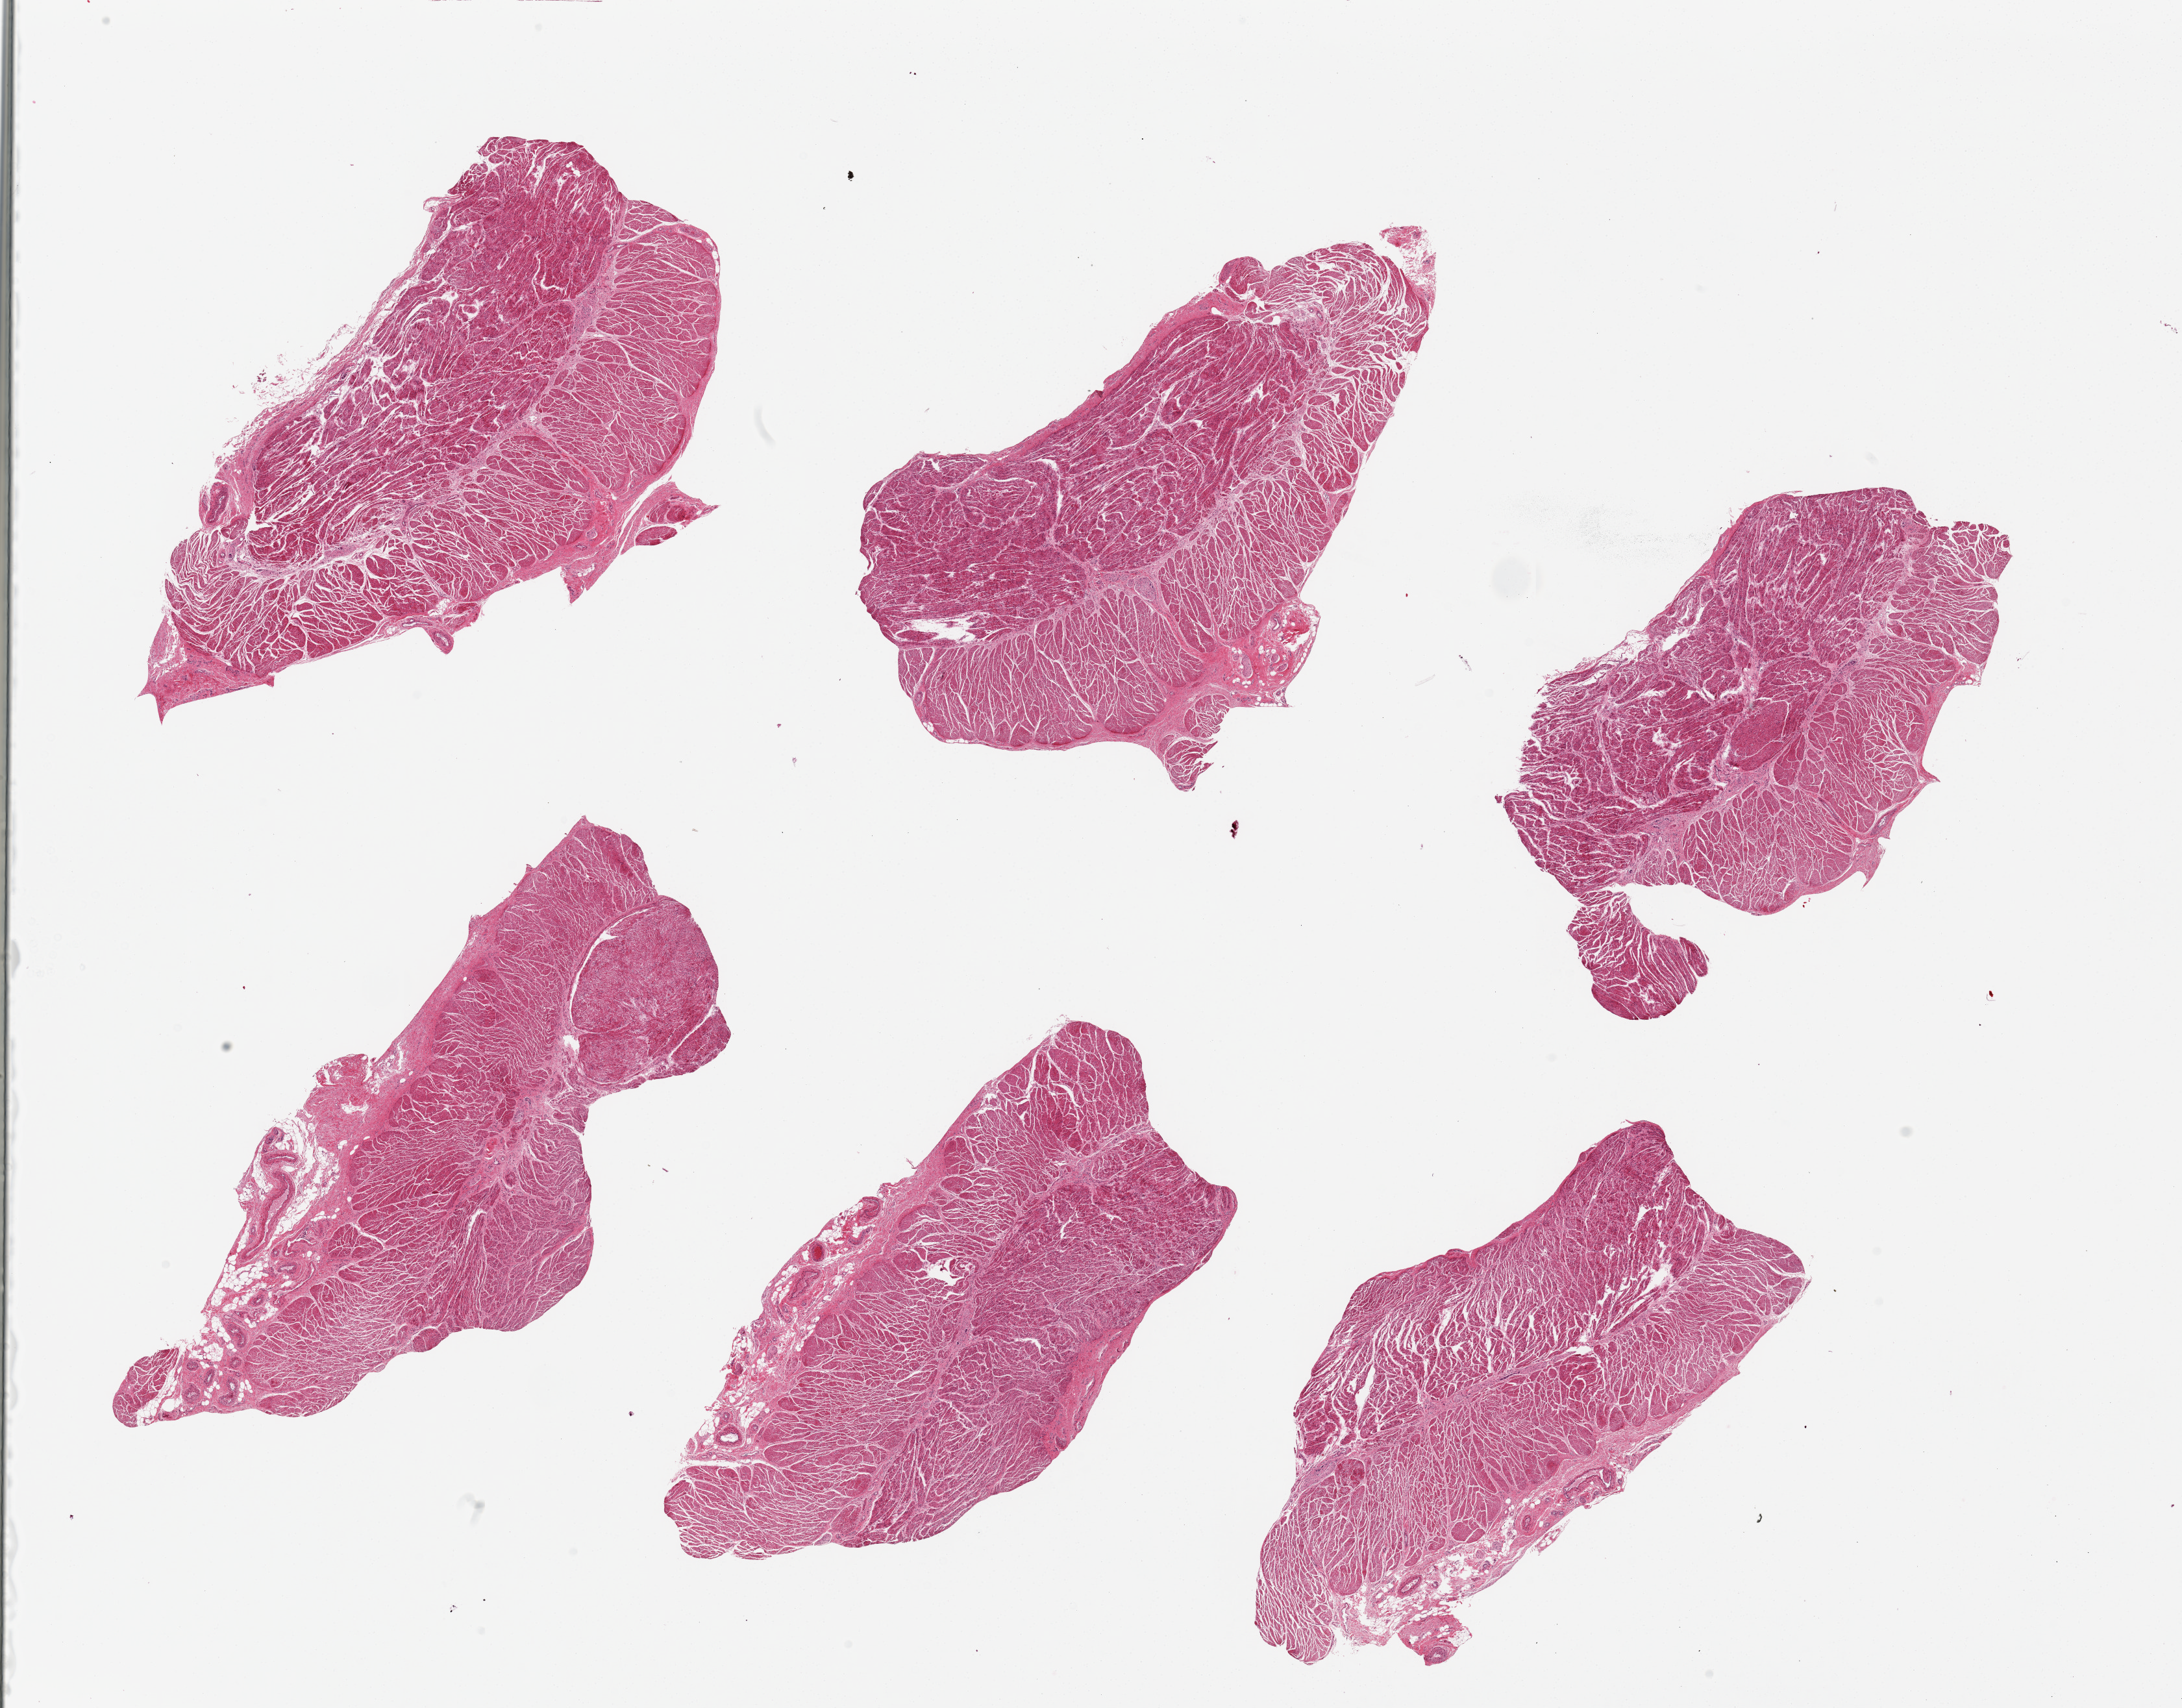
Digitized H&E-stained section — a low-resolution overview of the entire scanned area, about 26.6 x 20.8 mm (acquisition: 20x scan). PAXgene-fixed, paraffin-embedded tissue. Section of gastroesophageal junction (target tissue). Tissue donor sample. Donor sex: female.
- review note (as recorded): 6 pieces, all muscularis, good specimens